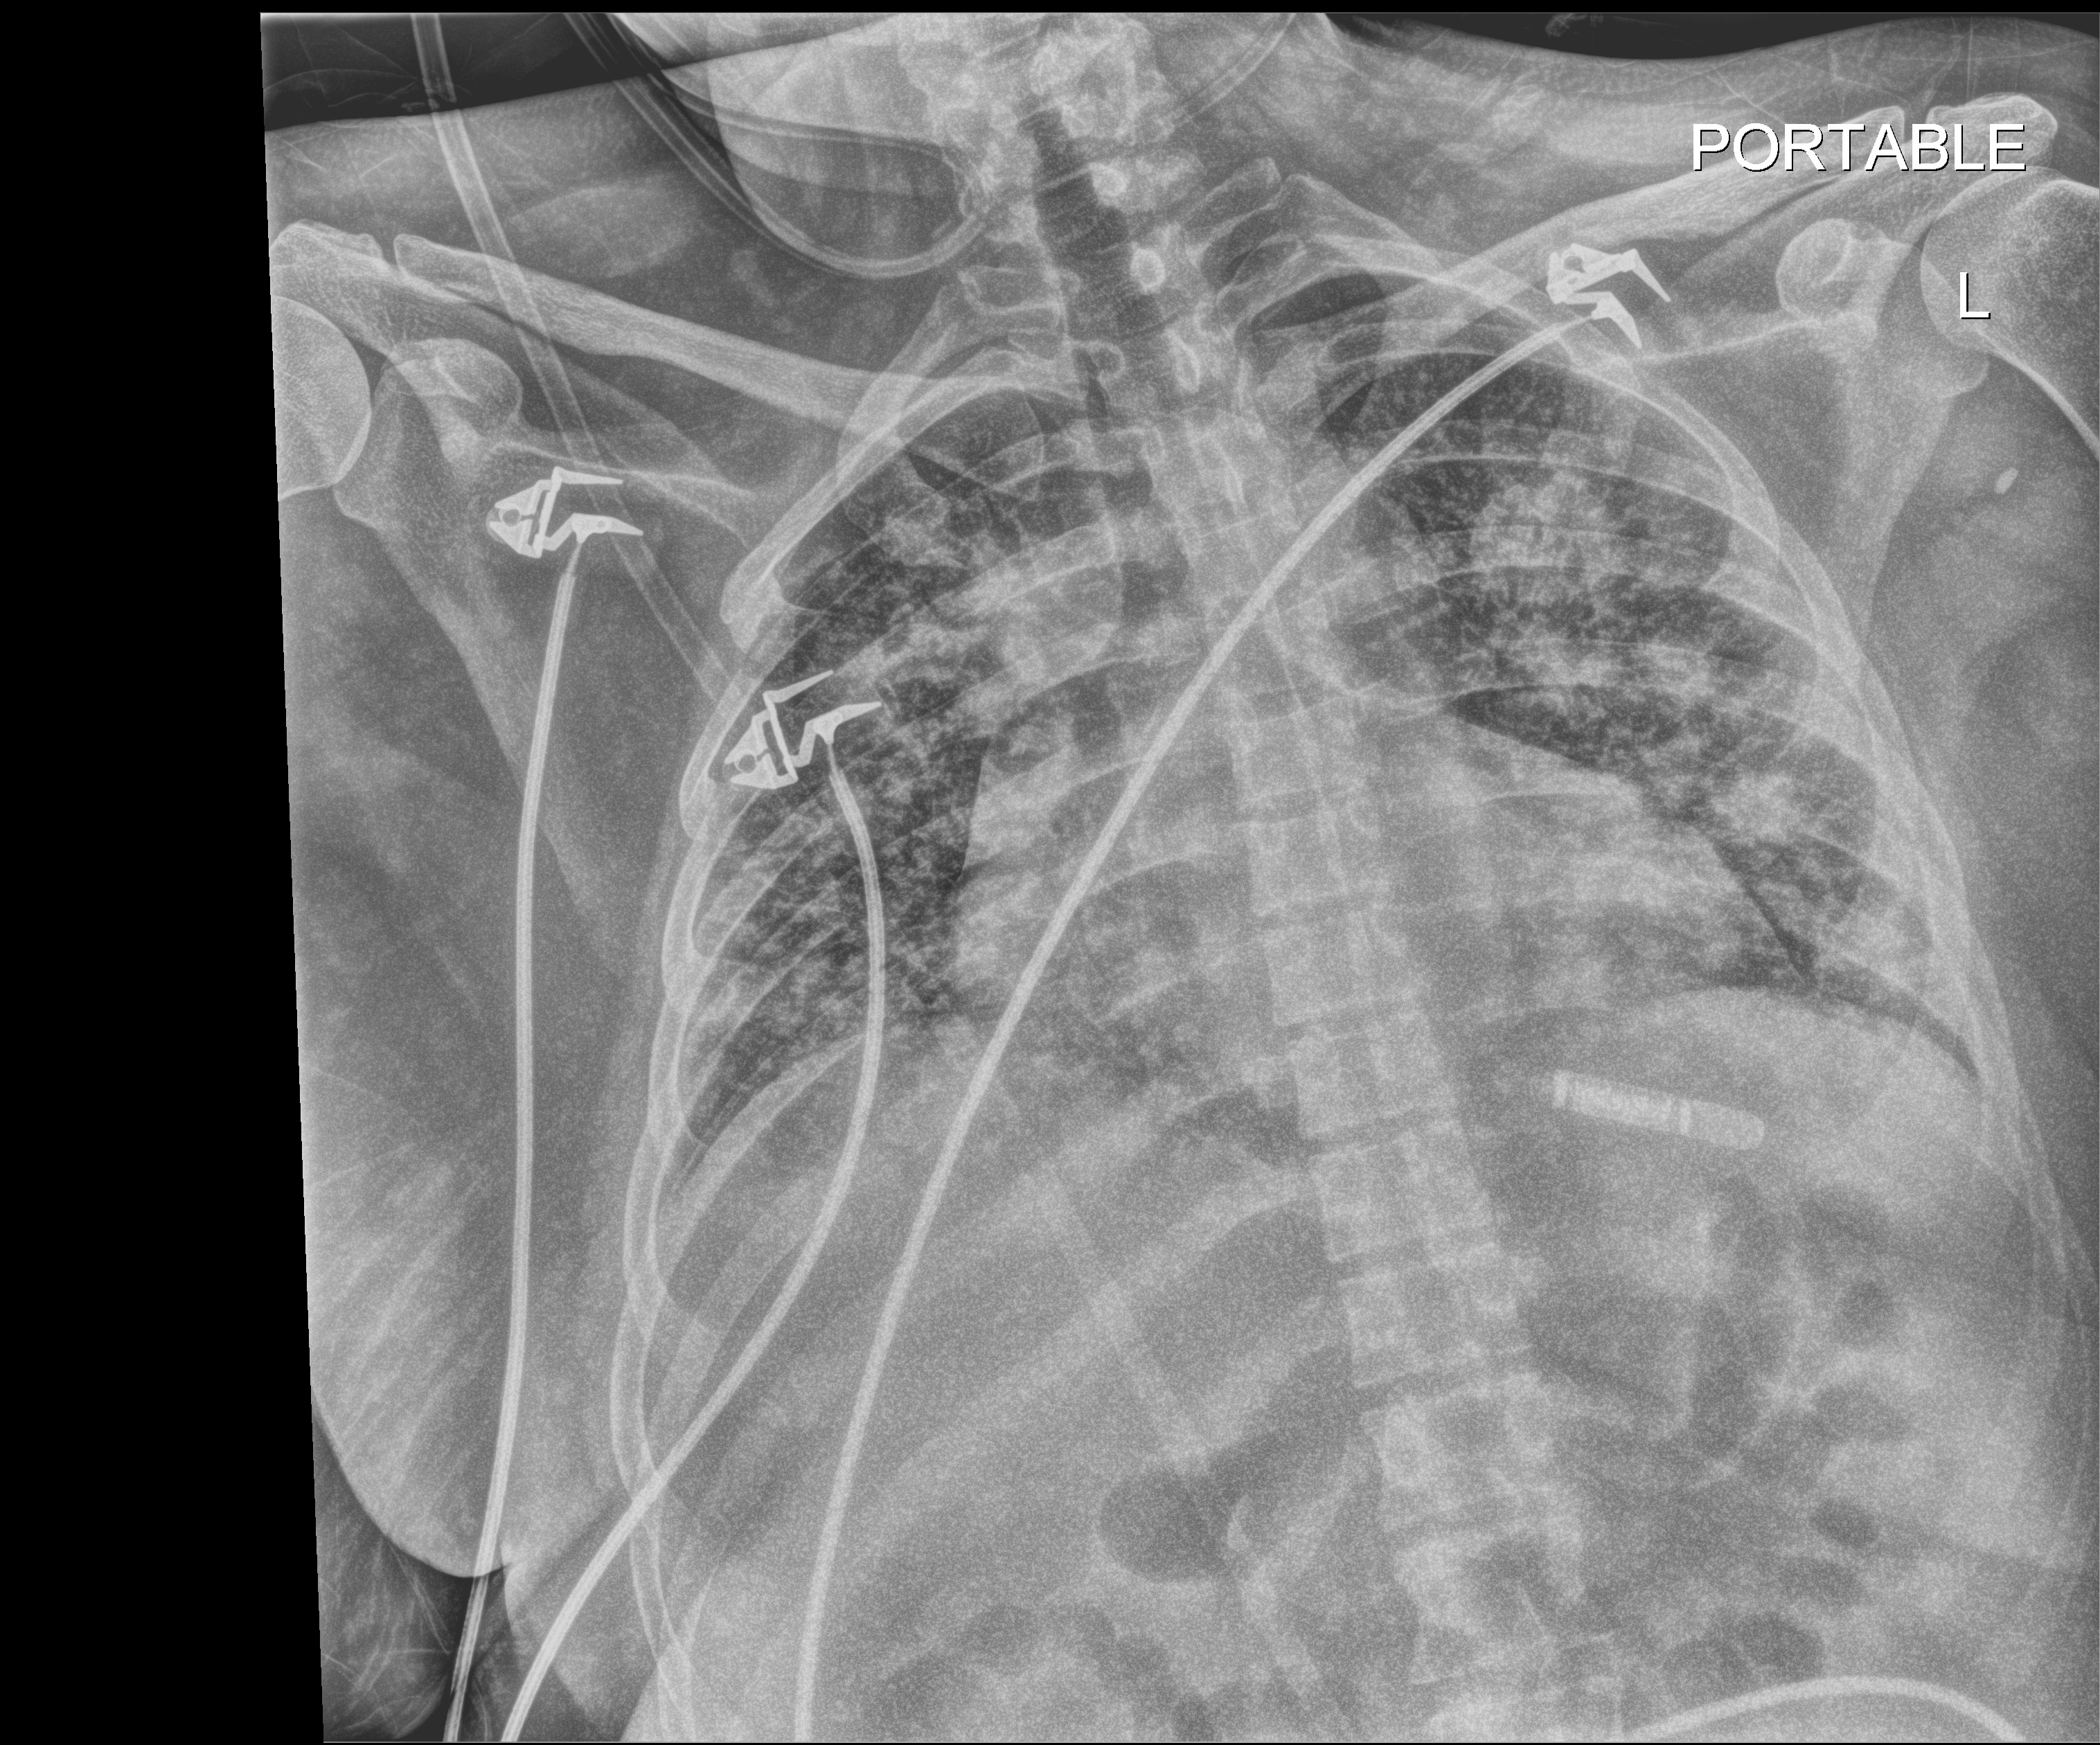
Bedside chest radiograph (digital radiography). Female patient hospitalised with COVID-19, age 18–59 years.
Hospital-stay facts (about this admission, not read from this image; timing relative to this image not recorded): length of hospital stay: 33 days.